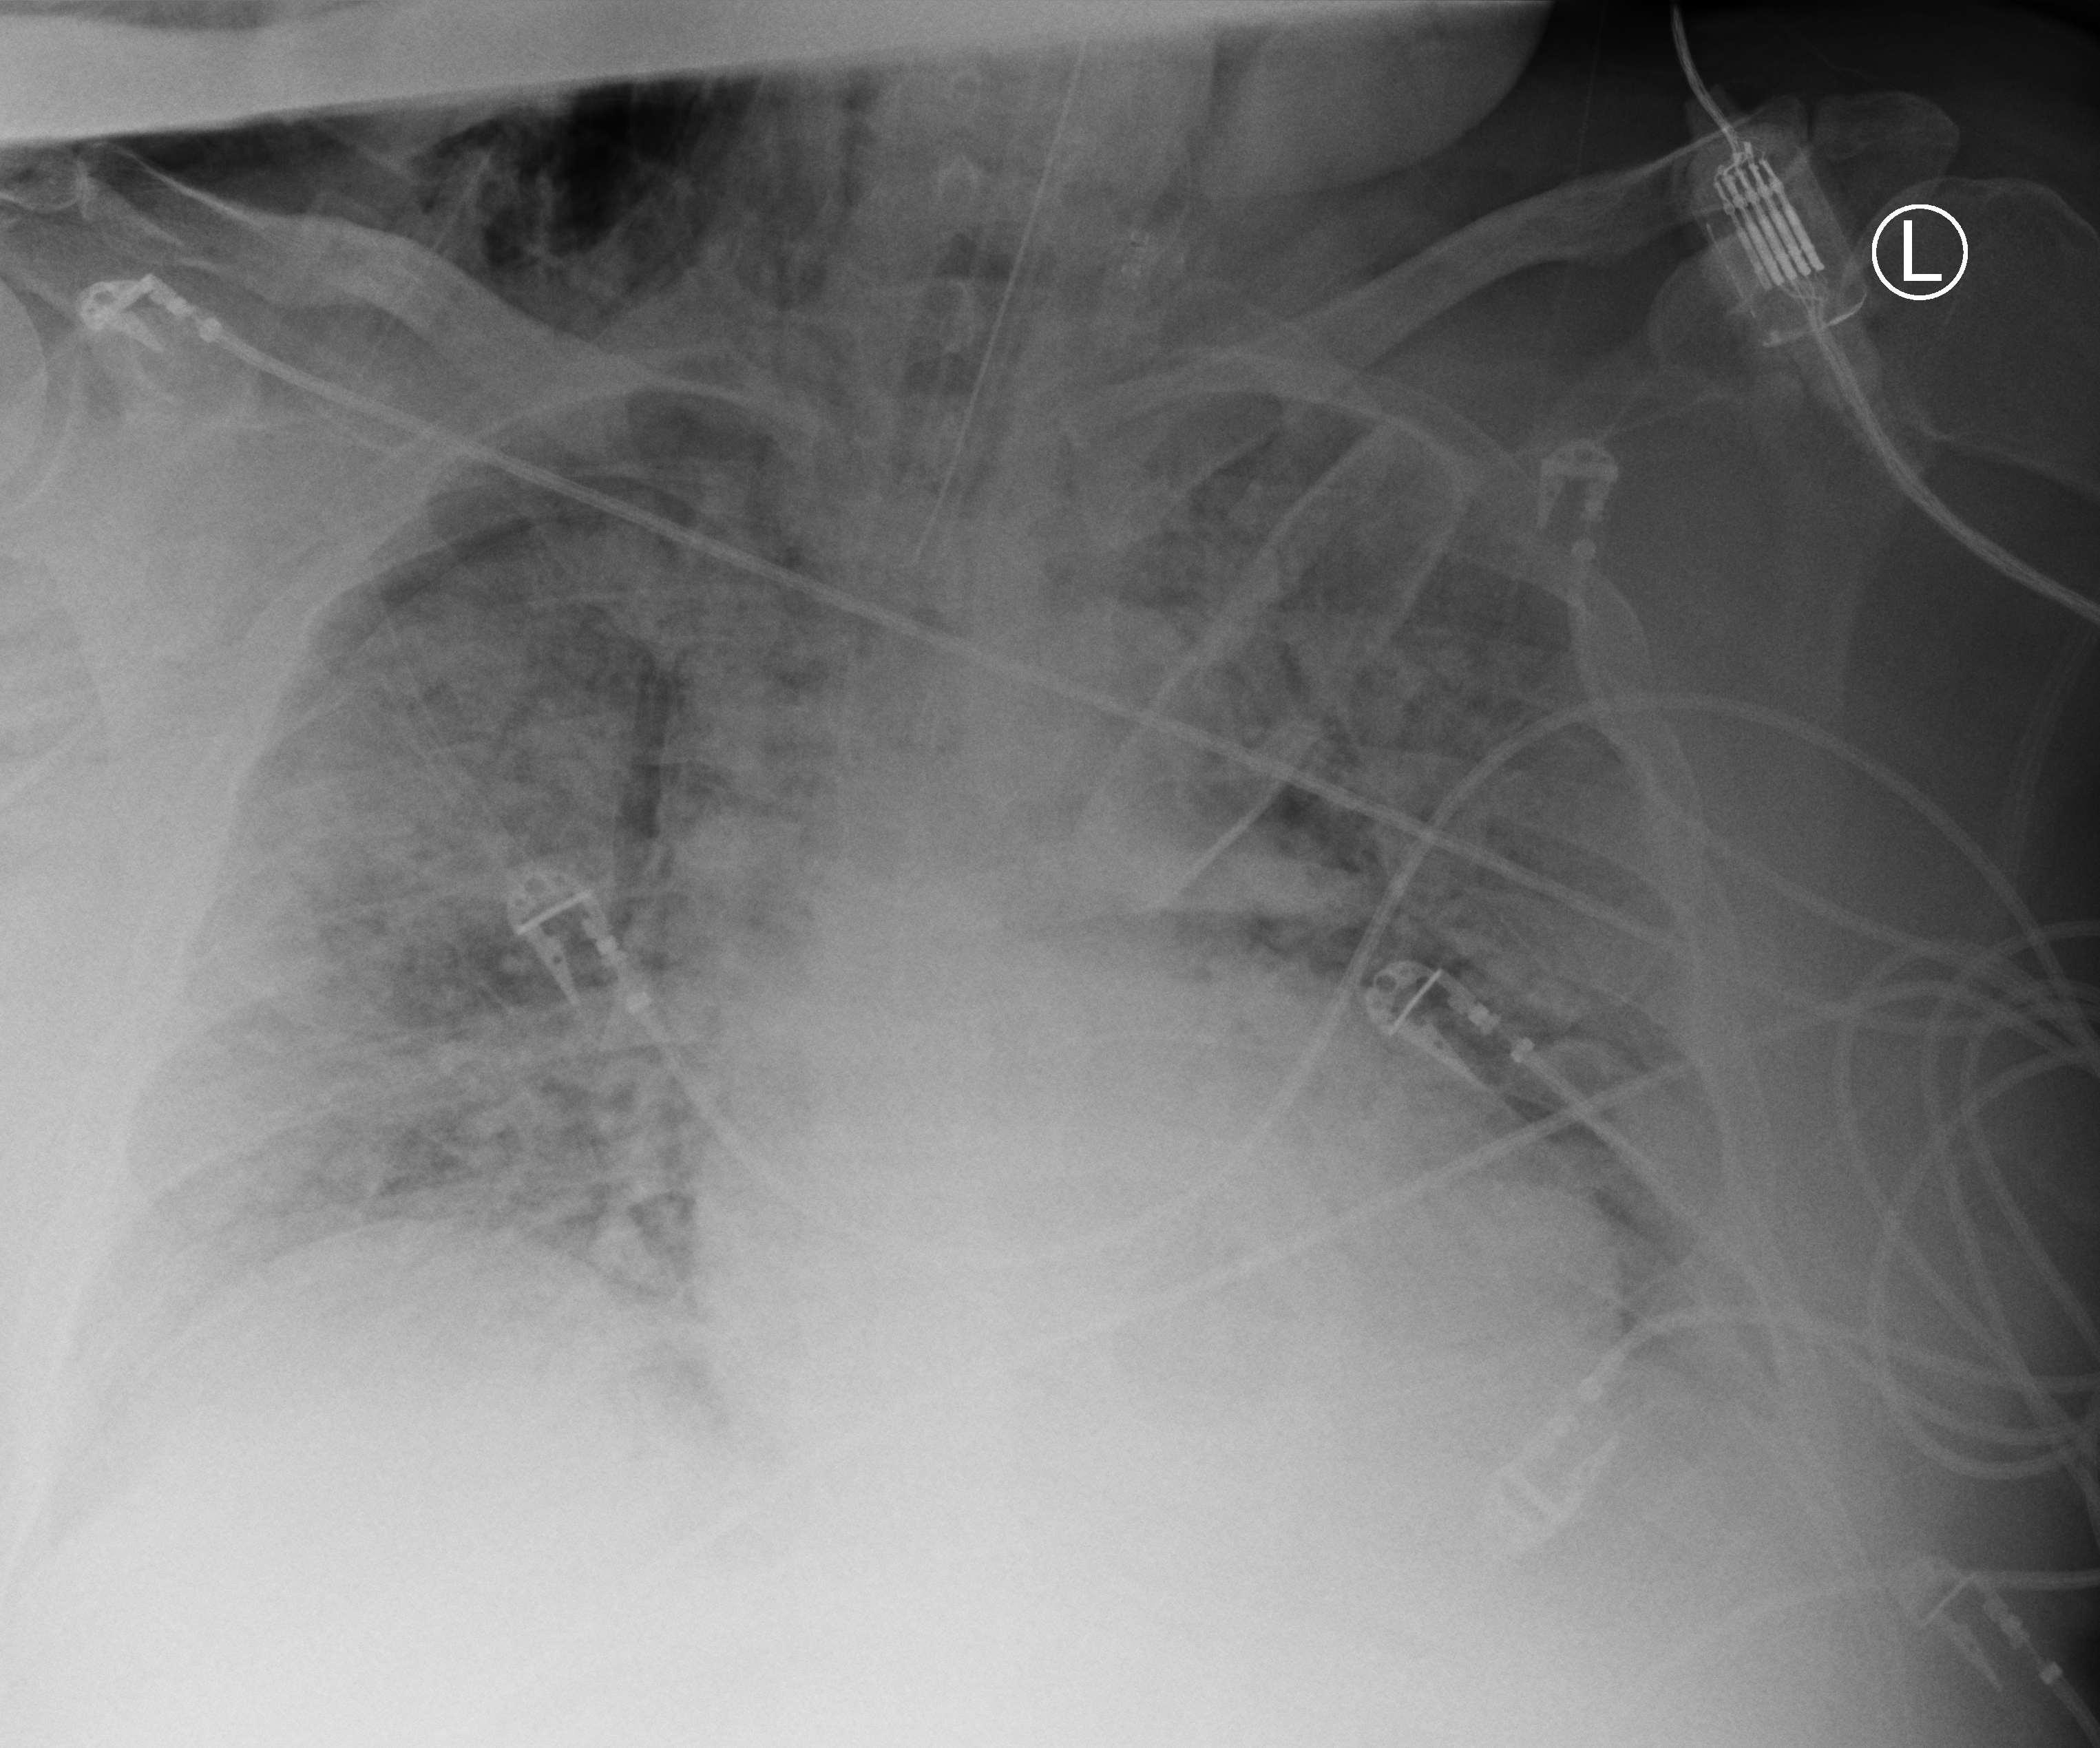
Portable chest radiograph; anteroposterior (AP) projection. Patient hospitalised with COVID-19, aged 18–59 years.
Admission-level facts for this patient (not findings on this image; timing relative to this image not recorded): admitted to intensive care during this hospital stay: yes; hypertension (admission record): yes; other chronic lung disease (admission record): no.